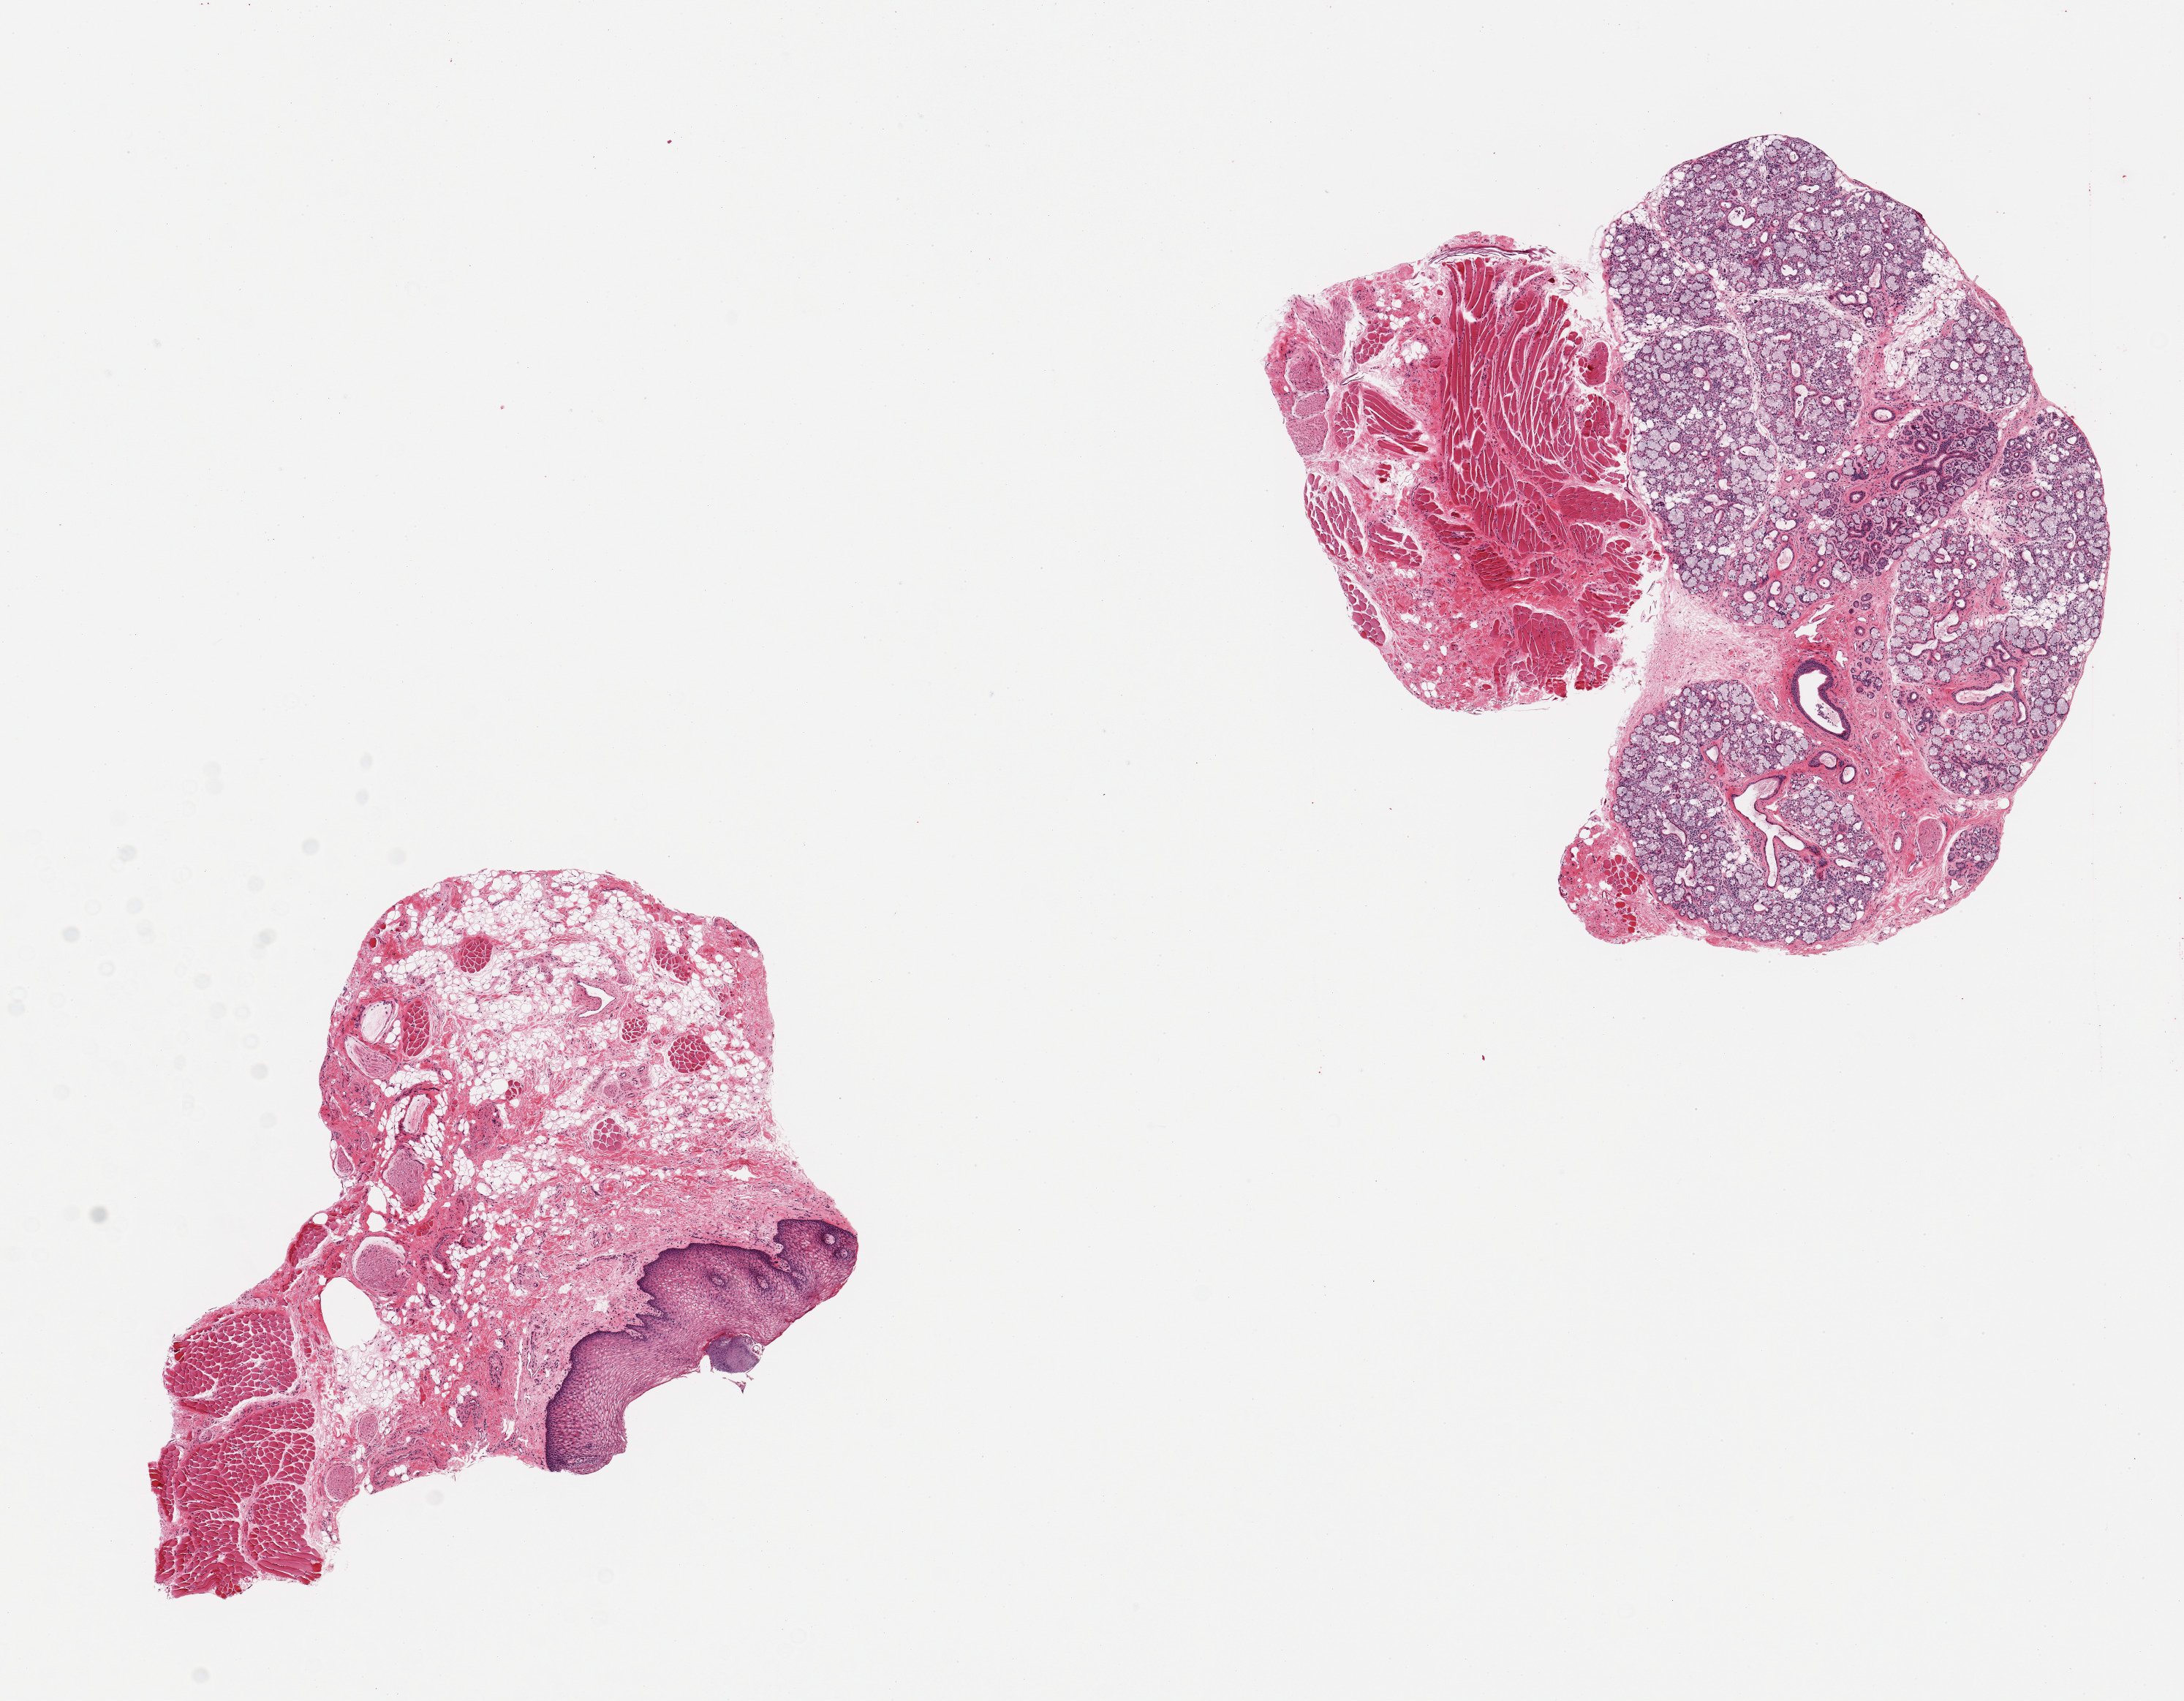
Whole-slide image, H&E stain, shown as a low-resolution overview of the whole scanned area (about 11.8 x 9.2 mm), PAXgene-fixed paraffin-embedded (PFPE) section, sampled site (target tissue): minor salivary gland, donor tissue sample. Donor: male.
- review note (as recorded): 2 pieces; one is 70% salivary gland with focal acute inflammation/30% skeletal muscle and nerve, second is all lip, nerve, skeletal muscle and fat